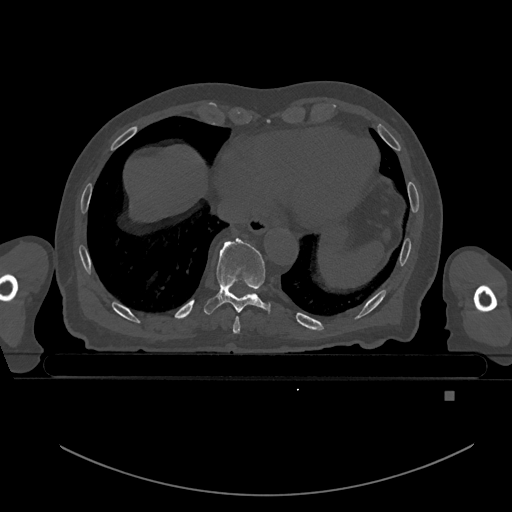
CT including the spine, one axial slice; position 147 of 969 along the scan axis; bone window (W 1800 / L 400 HU); 512 × 512 image matrix, field of view 456 × 456 mm. Male patient, age 82 years. From the clinical record (not read from this slice): primary cancer: prostate.
Annotated regions visible in this slice (semi-automatically segmented with operator editing):
- T8 vertebra: bounding box [x1, y1, x2, y2] px = [233, 317, 240, 334]
- T9 vertebra: [204, 238, 271, 315]